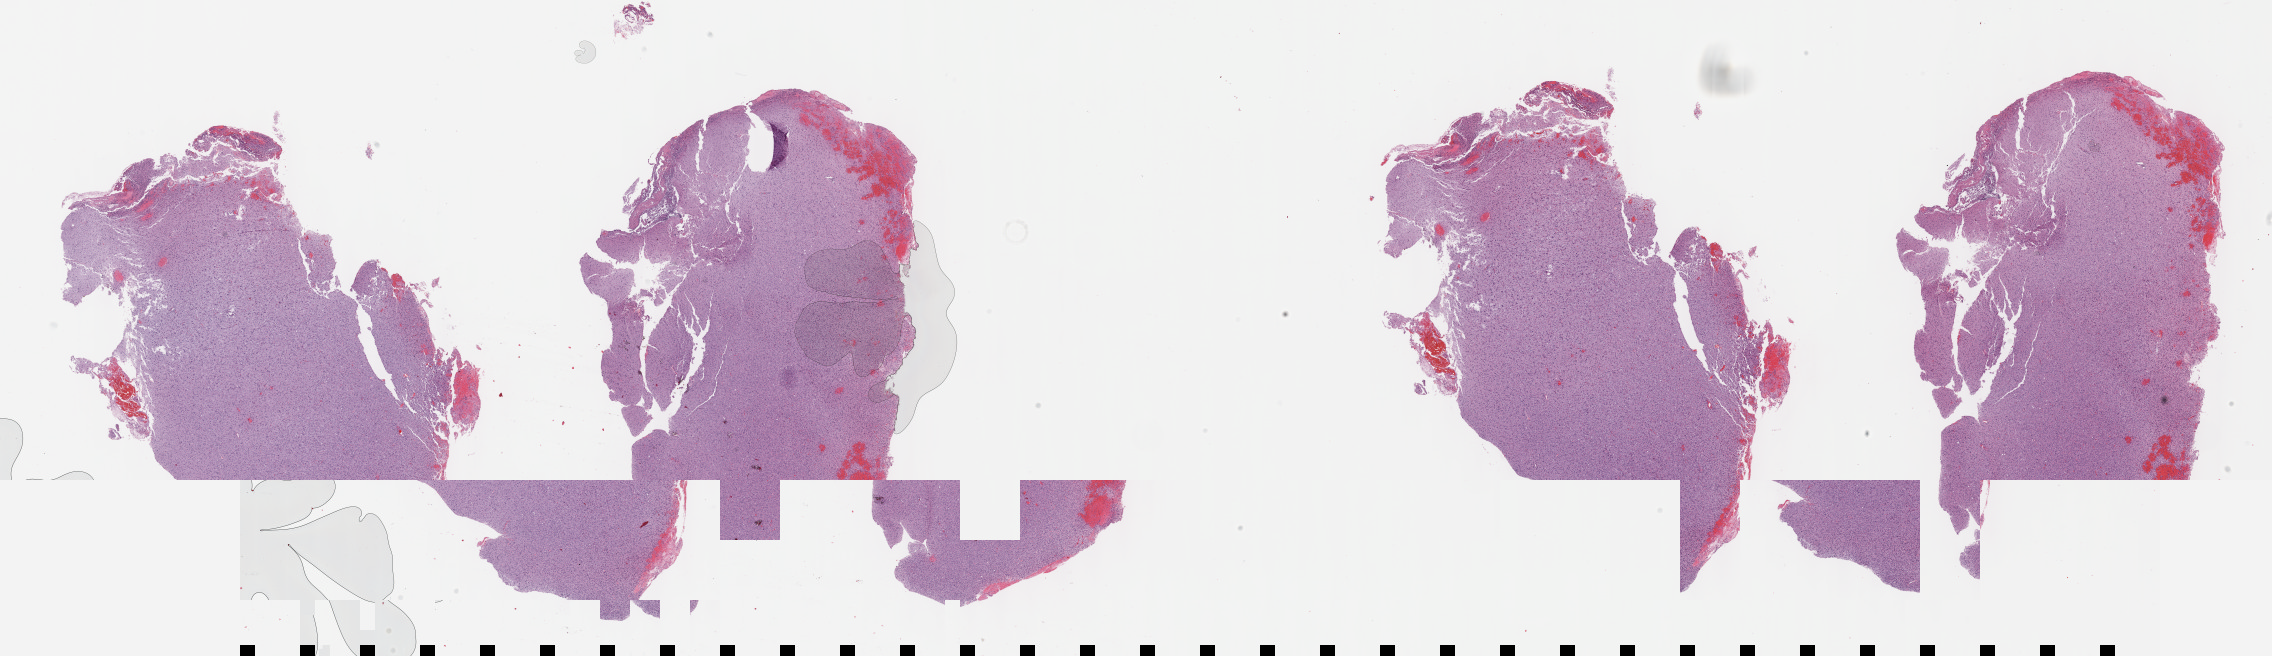
Digitized Hematoxylin and eosin (H&E) stained tissue section (whole slide), whole scanned area (about 36.7 x 10.6 mm, from a 40x scan) shown as a low-resolution overview; FFPE section; sample: primary tumour, brain. Female patient; age at initial diagnosis 51 years. Histologic grade: G3 (poorly differentiated).
Histologic diagnosis: Astrocytoma, anaplastic (cerebrum).